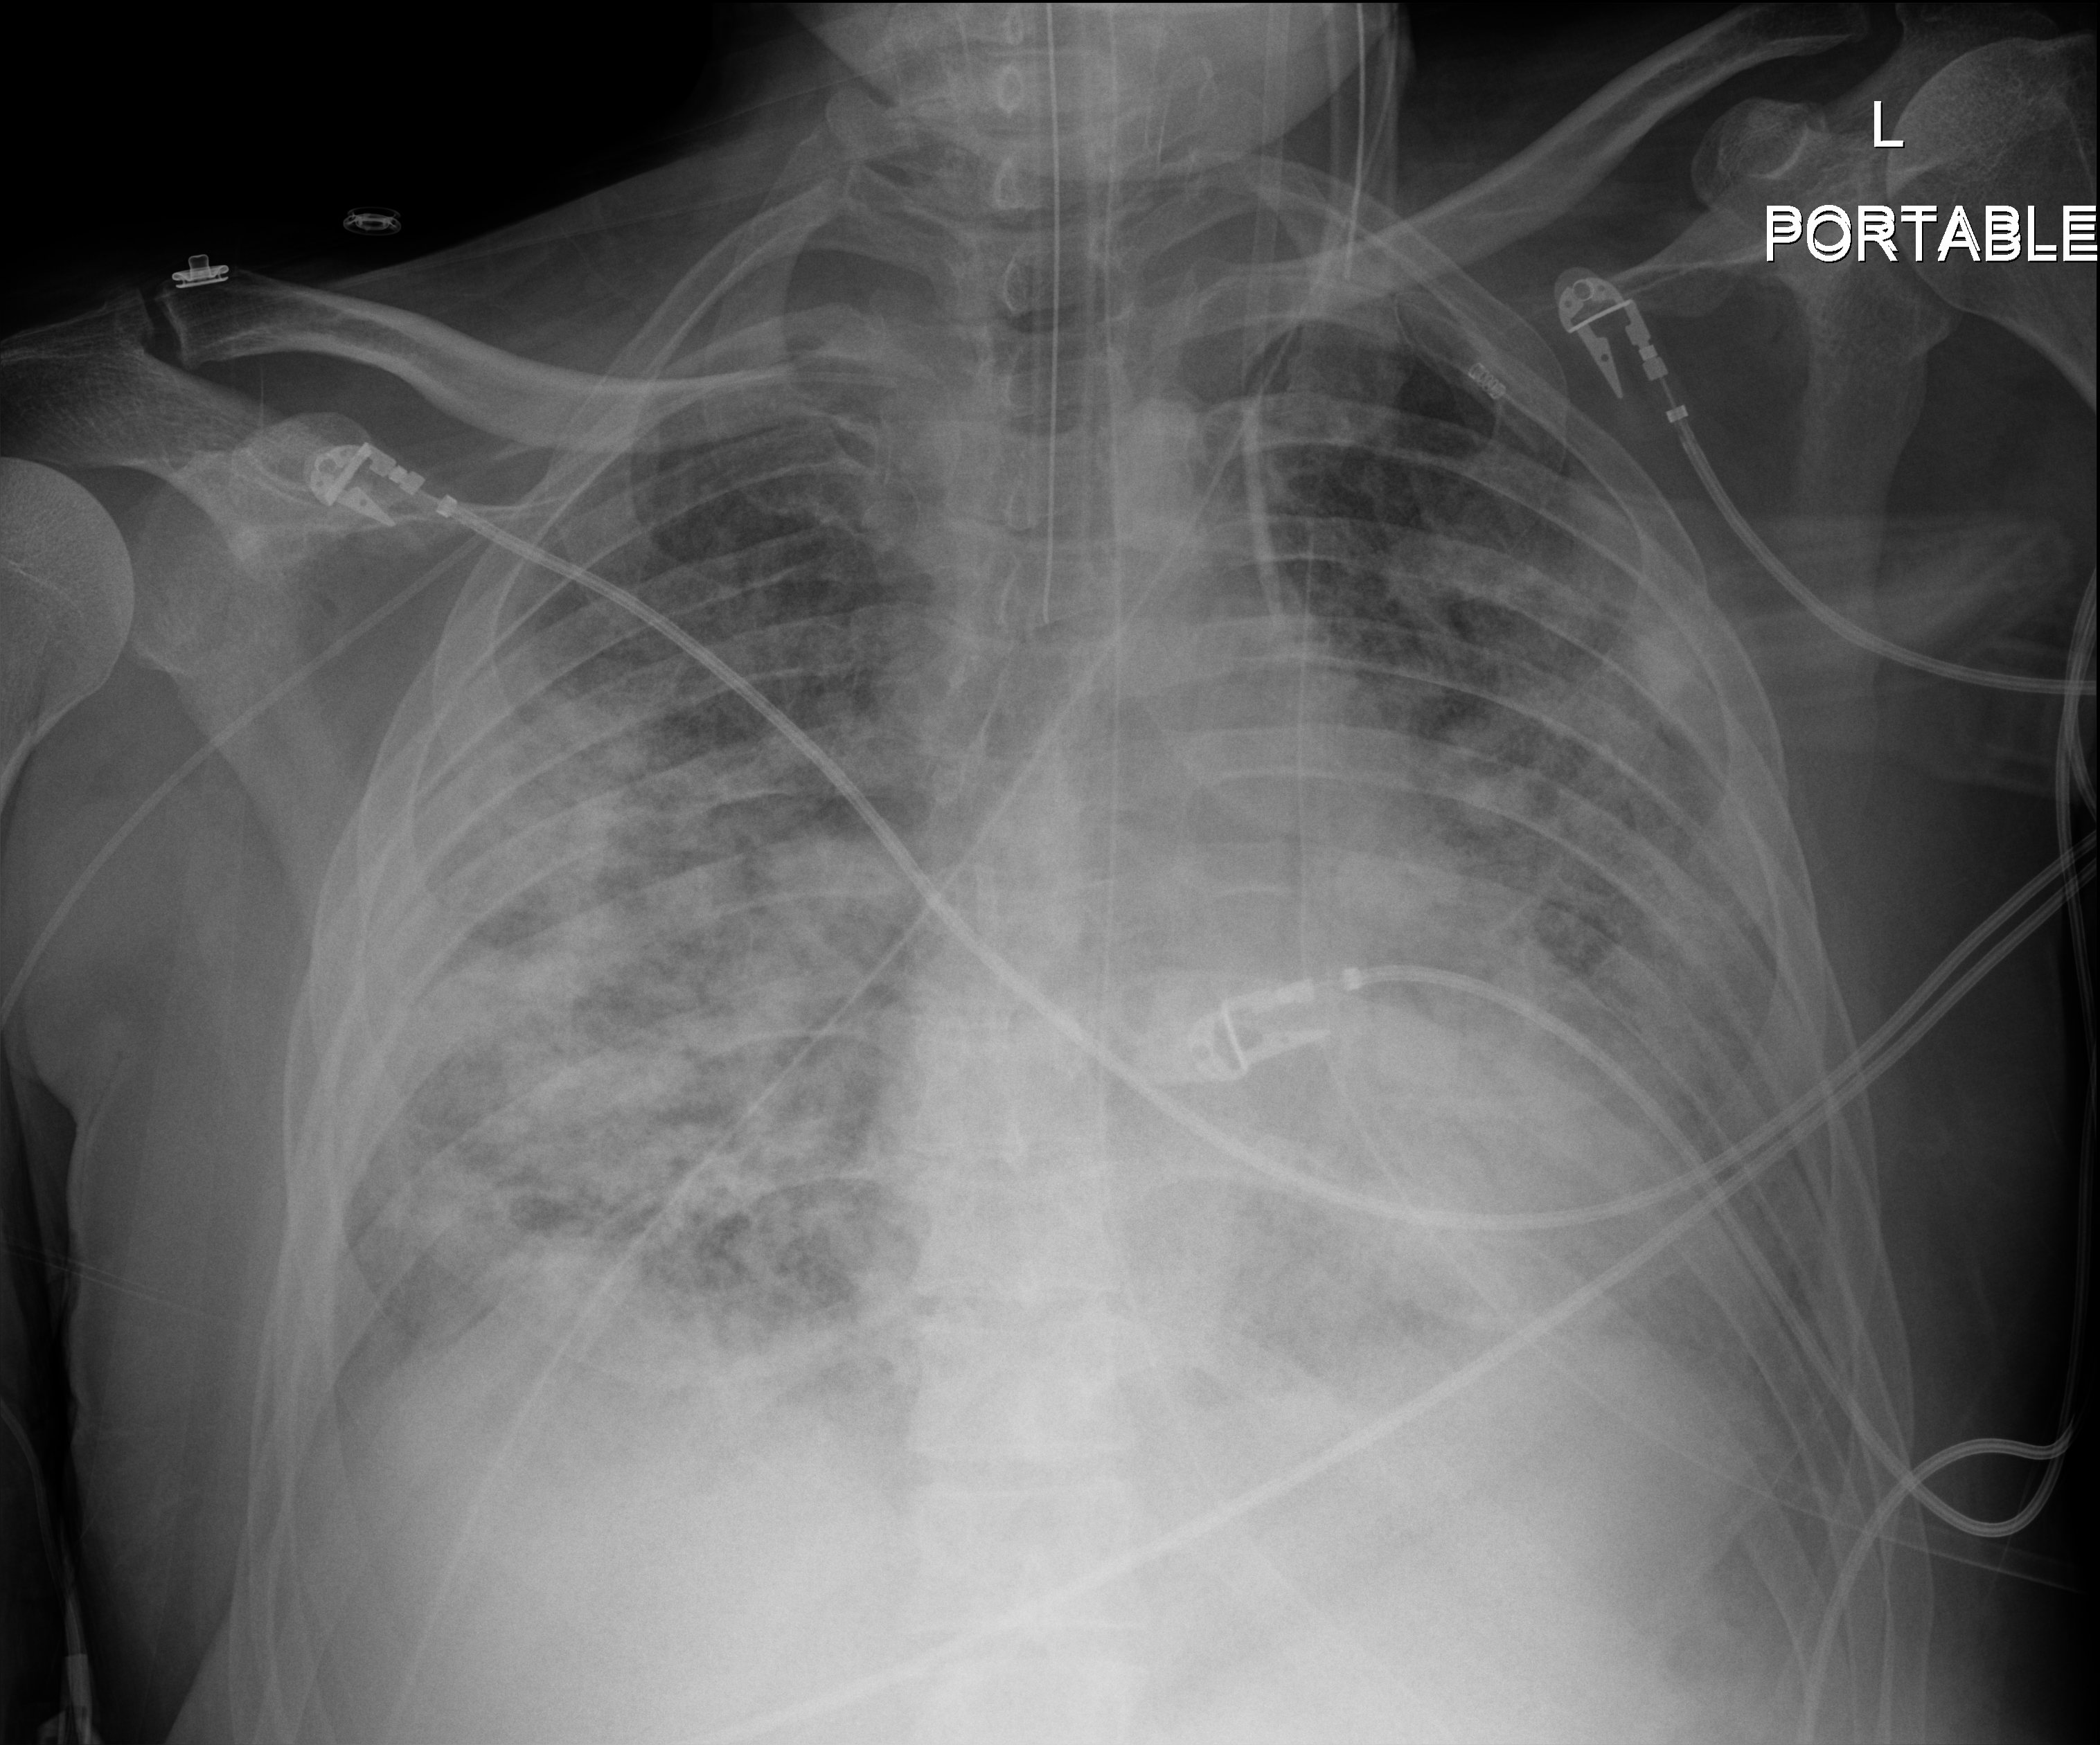
Chest X-ray; anteroposterior (AP) projection. Patient hospitalised with COVID-19; male, aged 18–59 years.
From the hospital-stay record, not from the radiograph (when in the stay this image was taken is not recorded): COPD (admission record): no; diabetes (admission record): no; mechanically ventilated during this hospital stay: yes.